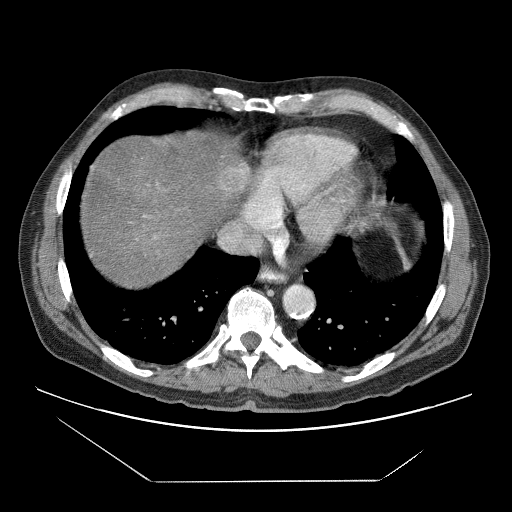
Contrast-enhanced abdominal CT (liver protocol), one axial slice; slice 68 of 83 in the series (ordered by position); reconstruction kernel STANDARD; 120 kVp; soft-tissue window (W 400 / L 40 HU); 512 × 512 image matrix. From the clinical record (not read from this slice): diagnosis: hepatocellular carcinoma (patient treated with transarterial chemoembolisation; whether this scan precedes or follows treatment is not stated here); TNM stage (as recorded): Stage-IVB.
Annotated regions visible in this slice (semi-automatic segmentation, software-assisted and operator-edited):
- liver parenchyma outside the tumour (the mass and vessels are separate outlines, so this box may not span the whole liver): bounding box (x1, y1, x2, y2) in pixels: (82, 136, 250, 286)
- mass: (217, 160, 248, 194)
- liver vessels: (143, 168, 249, 238)